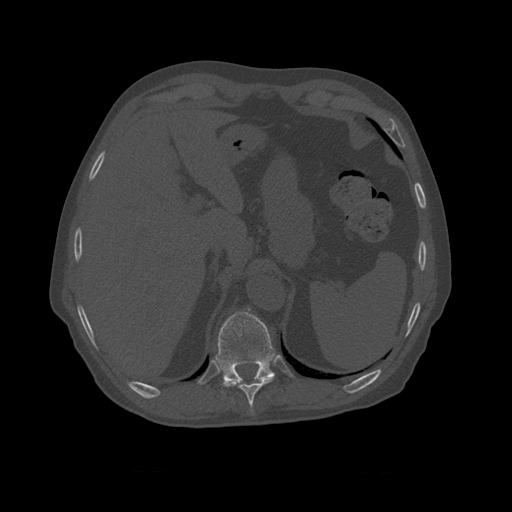
CT including the spine, one axial slice; slice 411 of 450 in the series (ordered by position); reconstruction kernel STANDARD; 120 kVp; bone window (W 1800 / L 400 HU); 512 × 512 image matrix. Patient age 75 years. Case-level facts recorded for this patient, not image findings: primary cancer: prostate.
Outlined on this slice (semi-automatically segmented with operator editing):
- T10 vertebra: bounding box (x1, y1, x2, y2) in pixels: (215, 310, 276, 393)
- T9 vertebra: (223, 379, 272, 410)